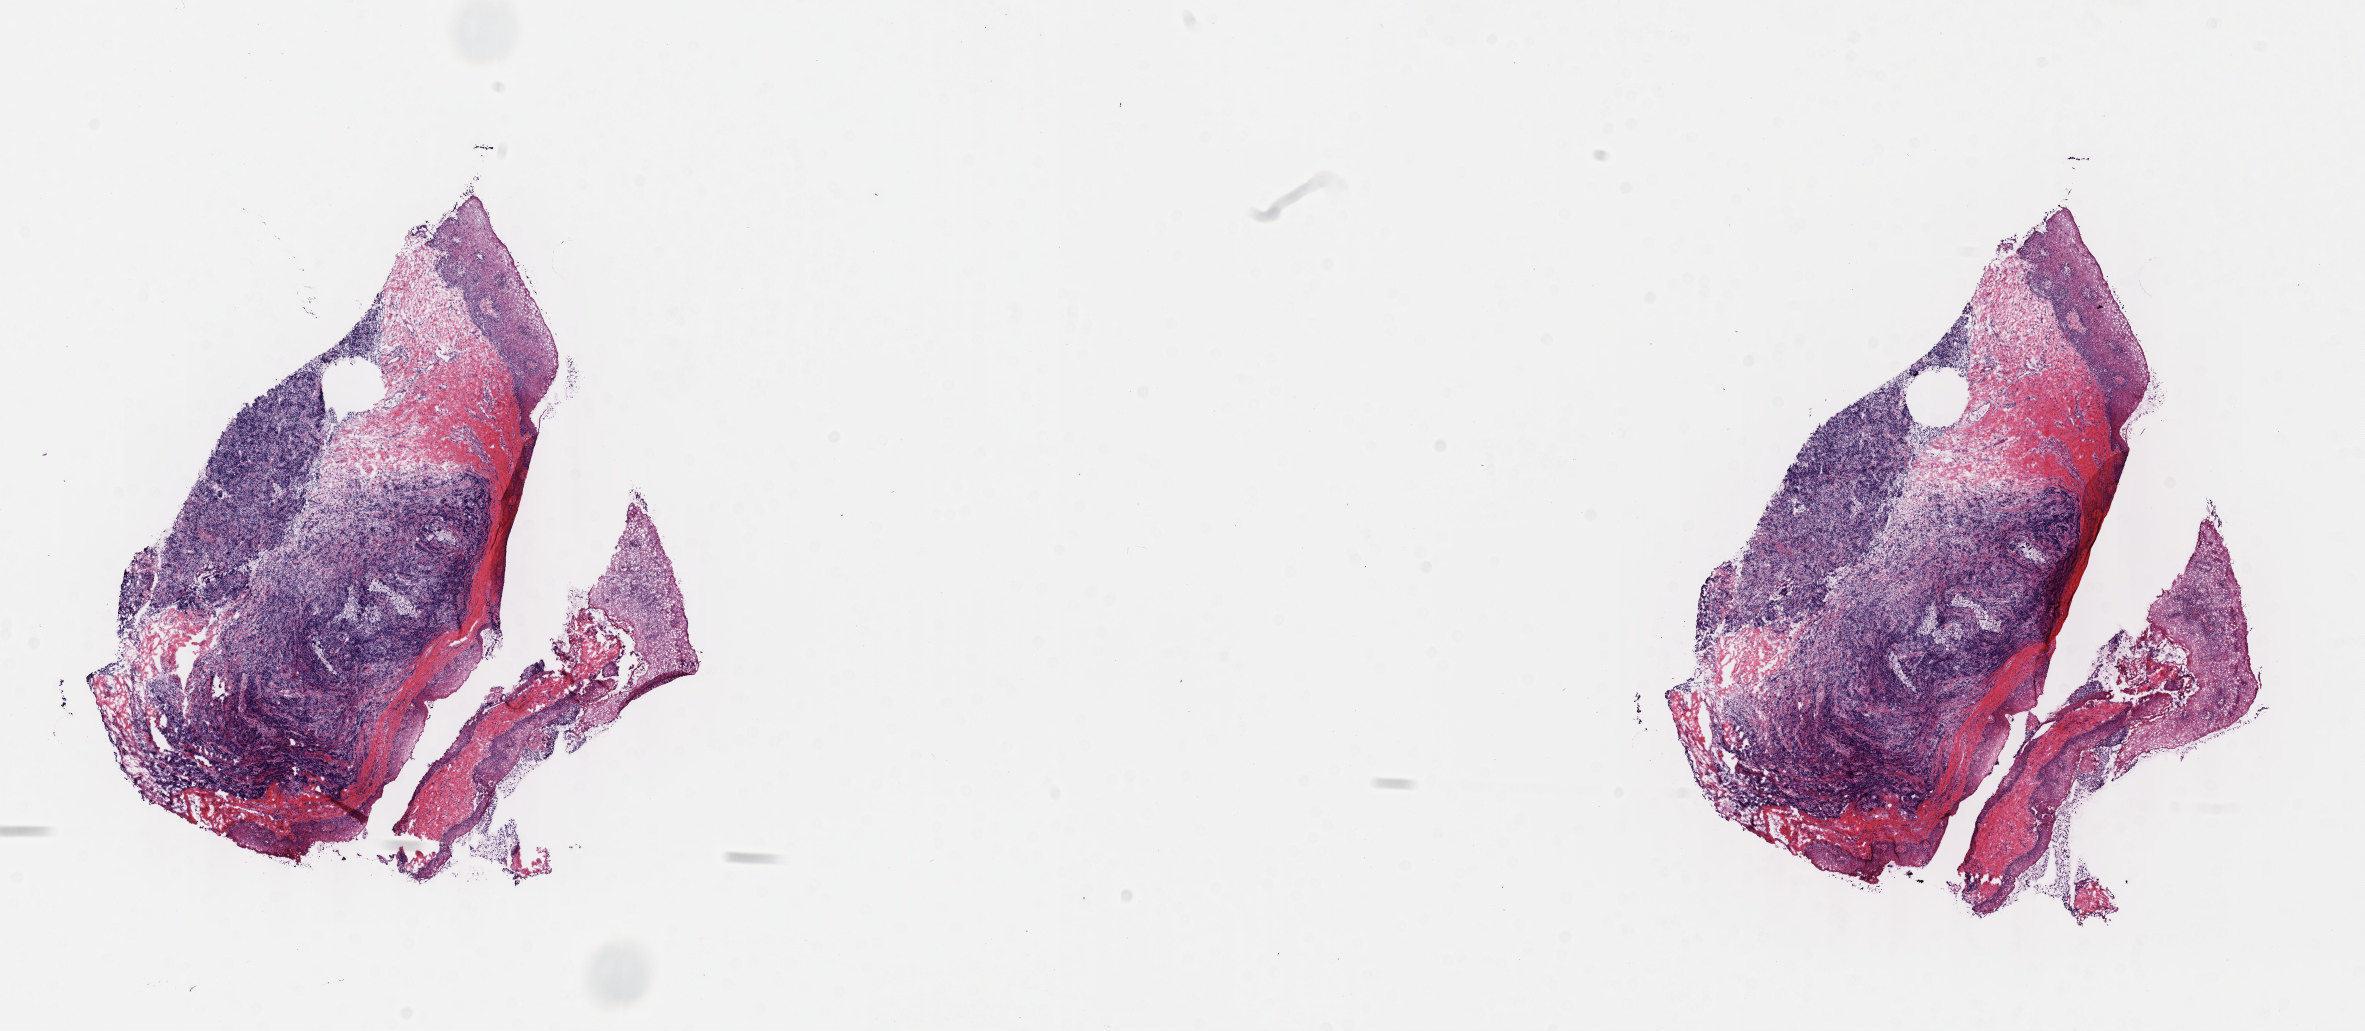
Digitized hematoxylin and eosin (H&E)-stained section — a low-resolution overview of the entire scanned area, about 19.1 x 8.3 mm. Cryosection. Specimen: primary tumor. Anatomic site: mandible. Male patient; age at initial diagnosis 9 years. Pathologist review of this section (percent, as recorded): tumor cells 70%, tumor nuclei 80%, stromal cells 15%, necrosis 15%, normal cells 0%. Infiltration values recorded for this section: lymphocyte infiltration 10%, monocyte infiltration 20%, neutrophil infiltration 5%.
- diagnosis: Burkitt lymphoma, NOS
- Ann Arbor stage (patient): Stage IV